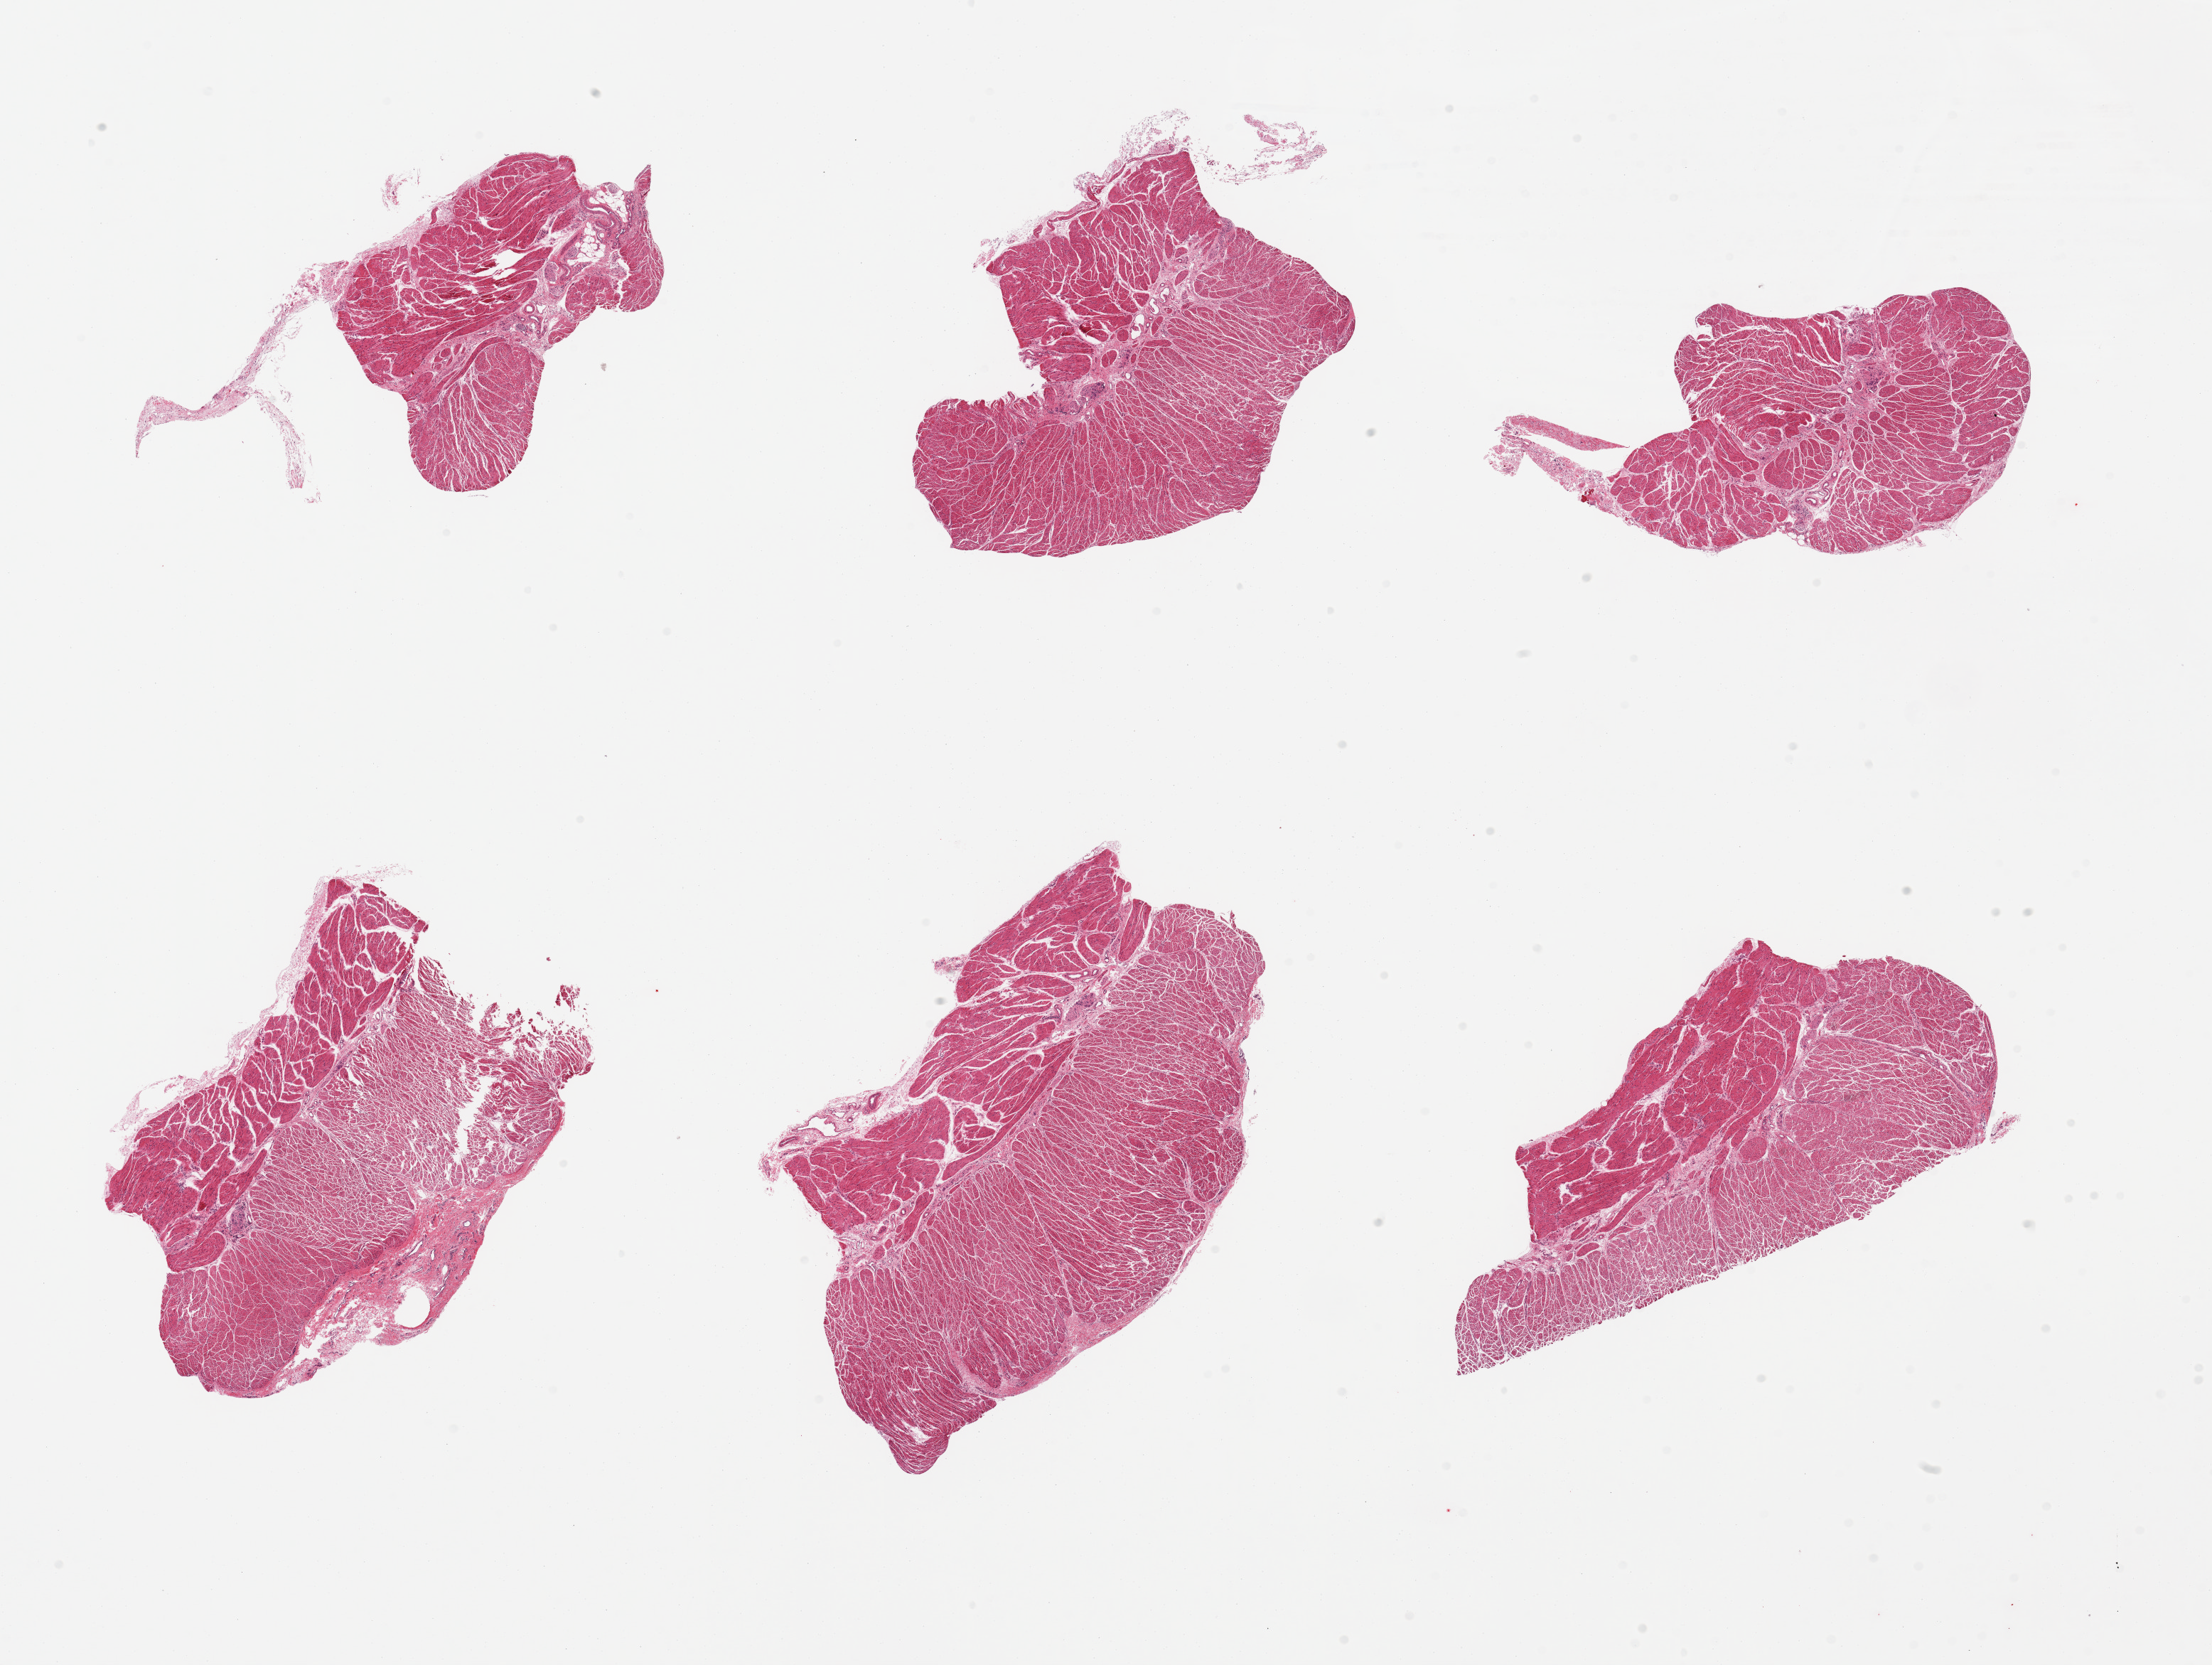
Haematoxylin and eosin whole-slide image, low-resolution overview of the scanned area, about 24.6 x 18.5 mm. PAXgene-fixed paraffin-embedded (PFPE) section. Target tissue: esophageal muscle. Tissue donor sample.
Review note (as recorded): 6 pieces; well trimmed.